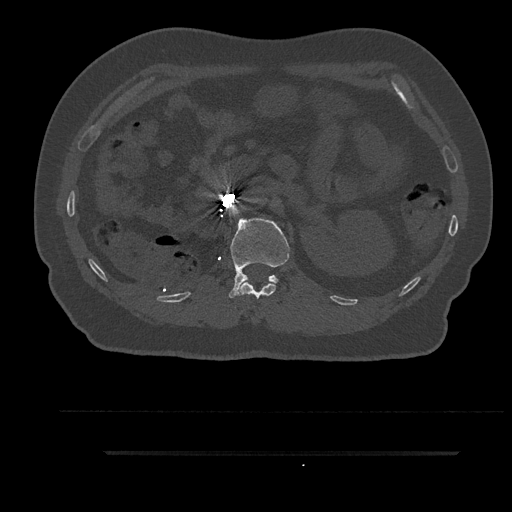
CT including the spine, one axial slice; position 199 of 797 along the scan axis; reconstruction kernel Br40s/3; 120 kVp; bone window (W 1800 / L 400 HU); 0.5 mm slice thickness; 512 × 512 image matrix, field of view 432 × 432 mm. Patient: male, 63 years. From the clinical record (not read from this slice): primary cancer: renal.
Structures marked on this image (semi-automatic segmentation, software-assisted and operator-edited):
- L1 vertebra: bounding box (x1, y1, x2, y2) in pixels: (229, 218, 290, 298)
- T12 vertebra: (239, 281, 276, 299)